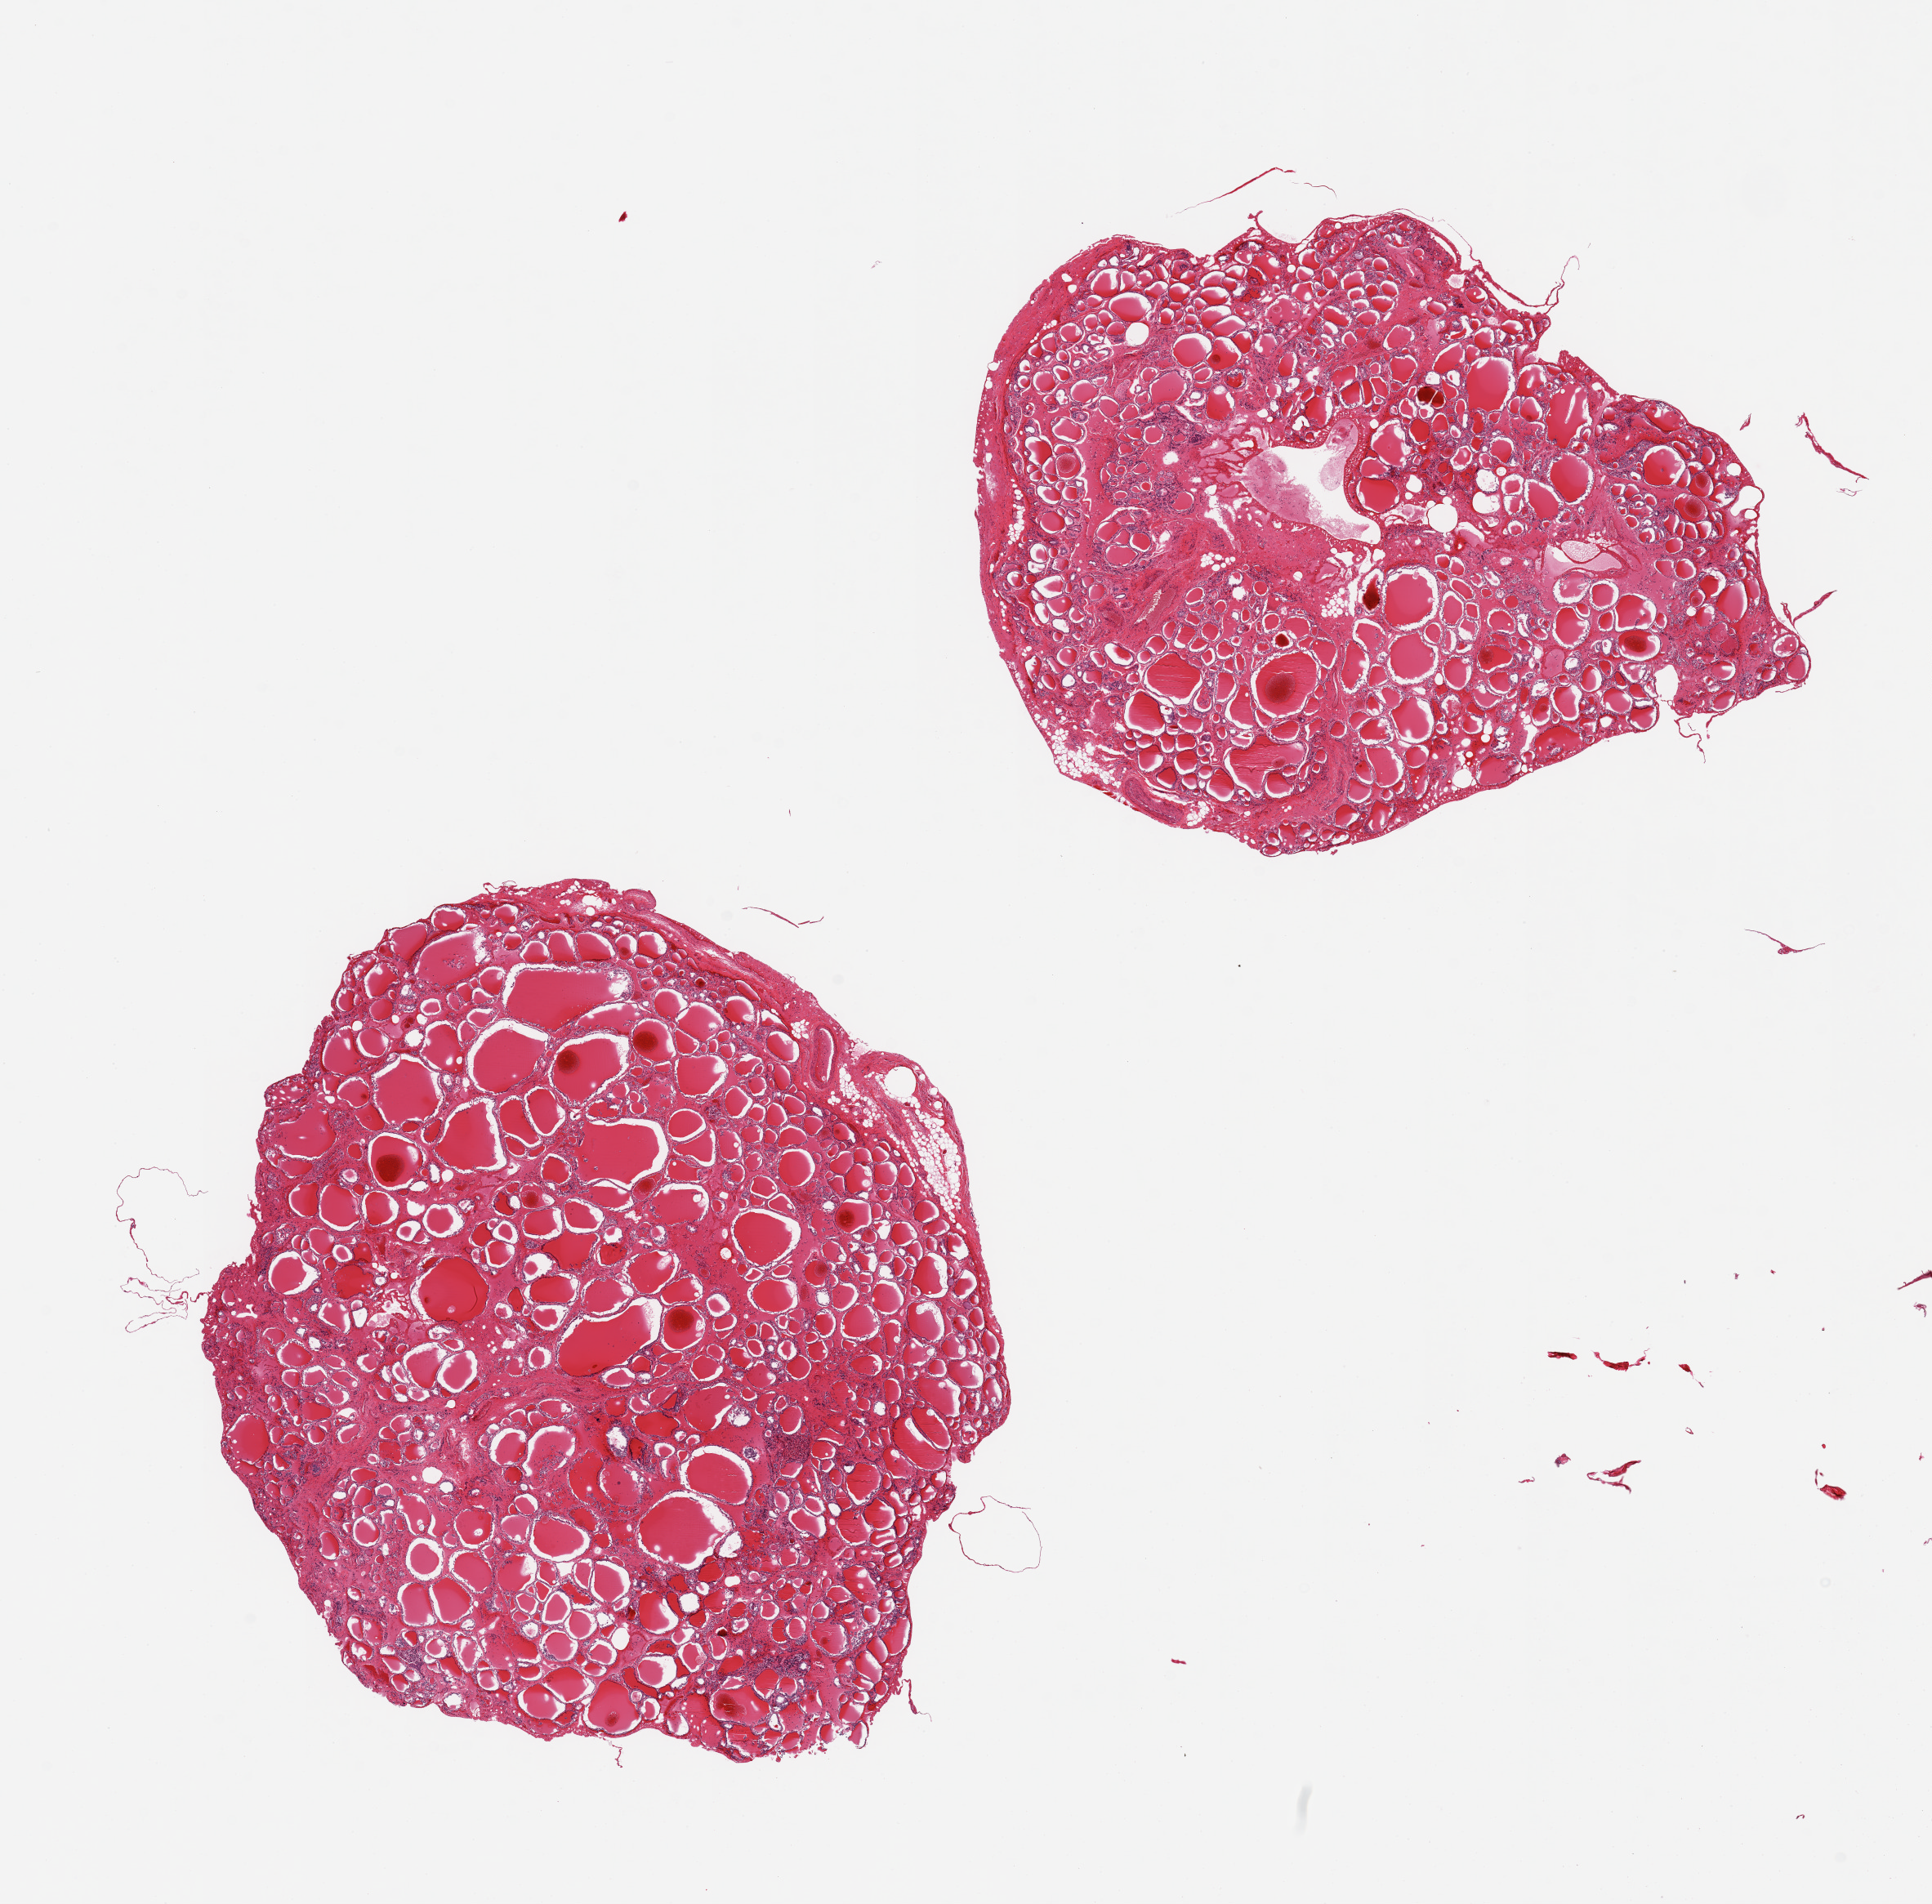
Haematoxylin and eosin whole-slide image, a low-resolution overview of the entire scanned area, about 18.7 x 18.4 mm (acquisition: 20x scan). PAXgene-fixed paraffin-embedded (PFPE) section. Sampled site (target tissue): thyroid. Tissue donor sample. Donor: male.
Pathologist's review note for this sample: 2 pieces.